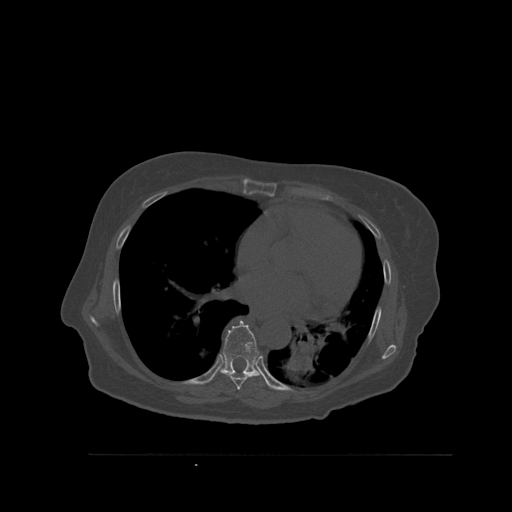
CT including the spine, one axial slice. Slice 357 of 527 in the series (ordered by position). Bone window (W 1800 / L 400 HU). 1.5 mm slice thickness. 512 × 512 image matrix, field of view 470 × 470 mm. Female patient, age 73 years. From the clinical record (not read from this slice): primary cancer: breast.
Outlined on this slice (semi-automatic segmentation, software-assisted and operator-edited):
- T7 vertebra: bounding box [x1, y1, x2, y2] px = [227, 374, 256, 390]
- T8 vertebra: [213, 320, 267, 386]